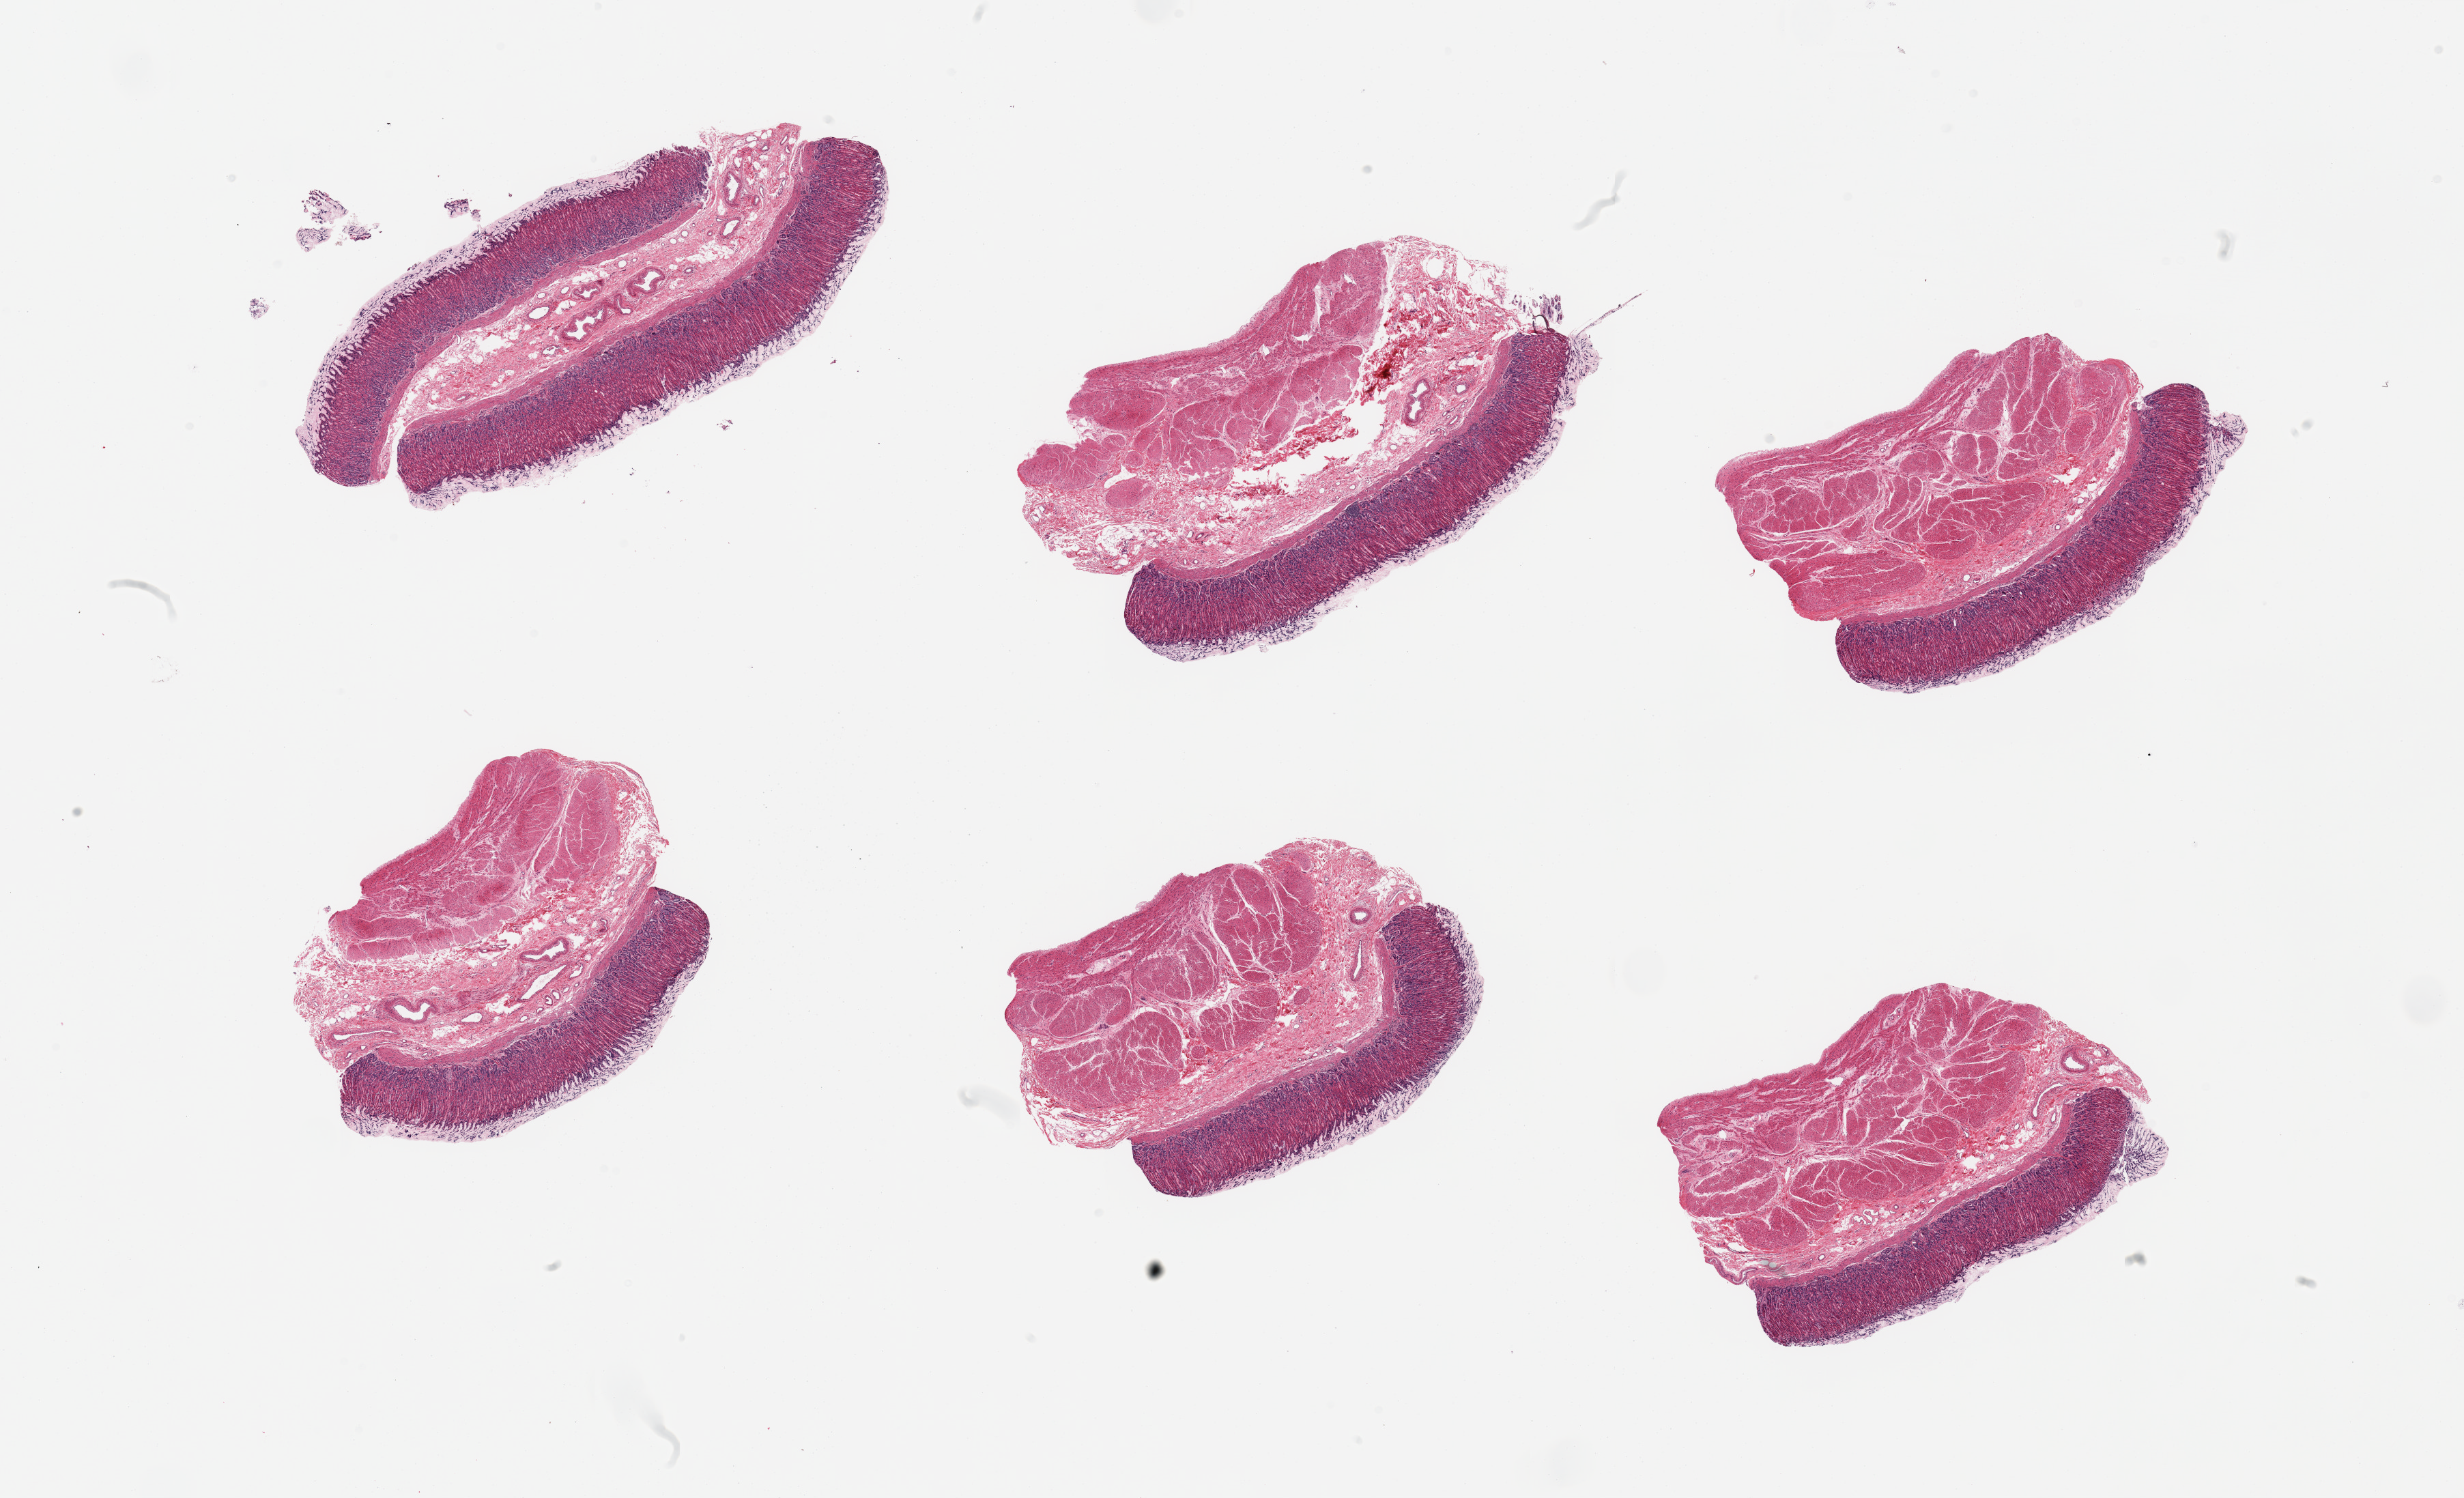
H&E whole-slide image, a low-resolution overview of the entire scanned area, about 28.5 x 17.4 mm (acquisition: 20x scan); PAXgene-fixed, paraffin-embedded tissue; target tissue: stomach; donor tissue sample.
- pathologist's review note for this sample: 6 pieces; 5 are full thickness, well preserved, but with some sloughing of superficial glands